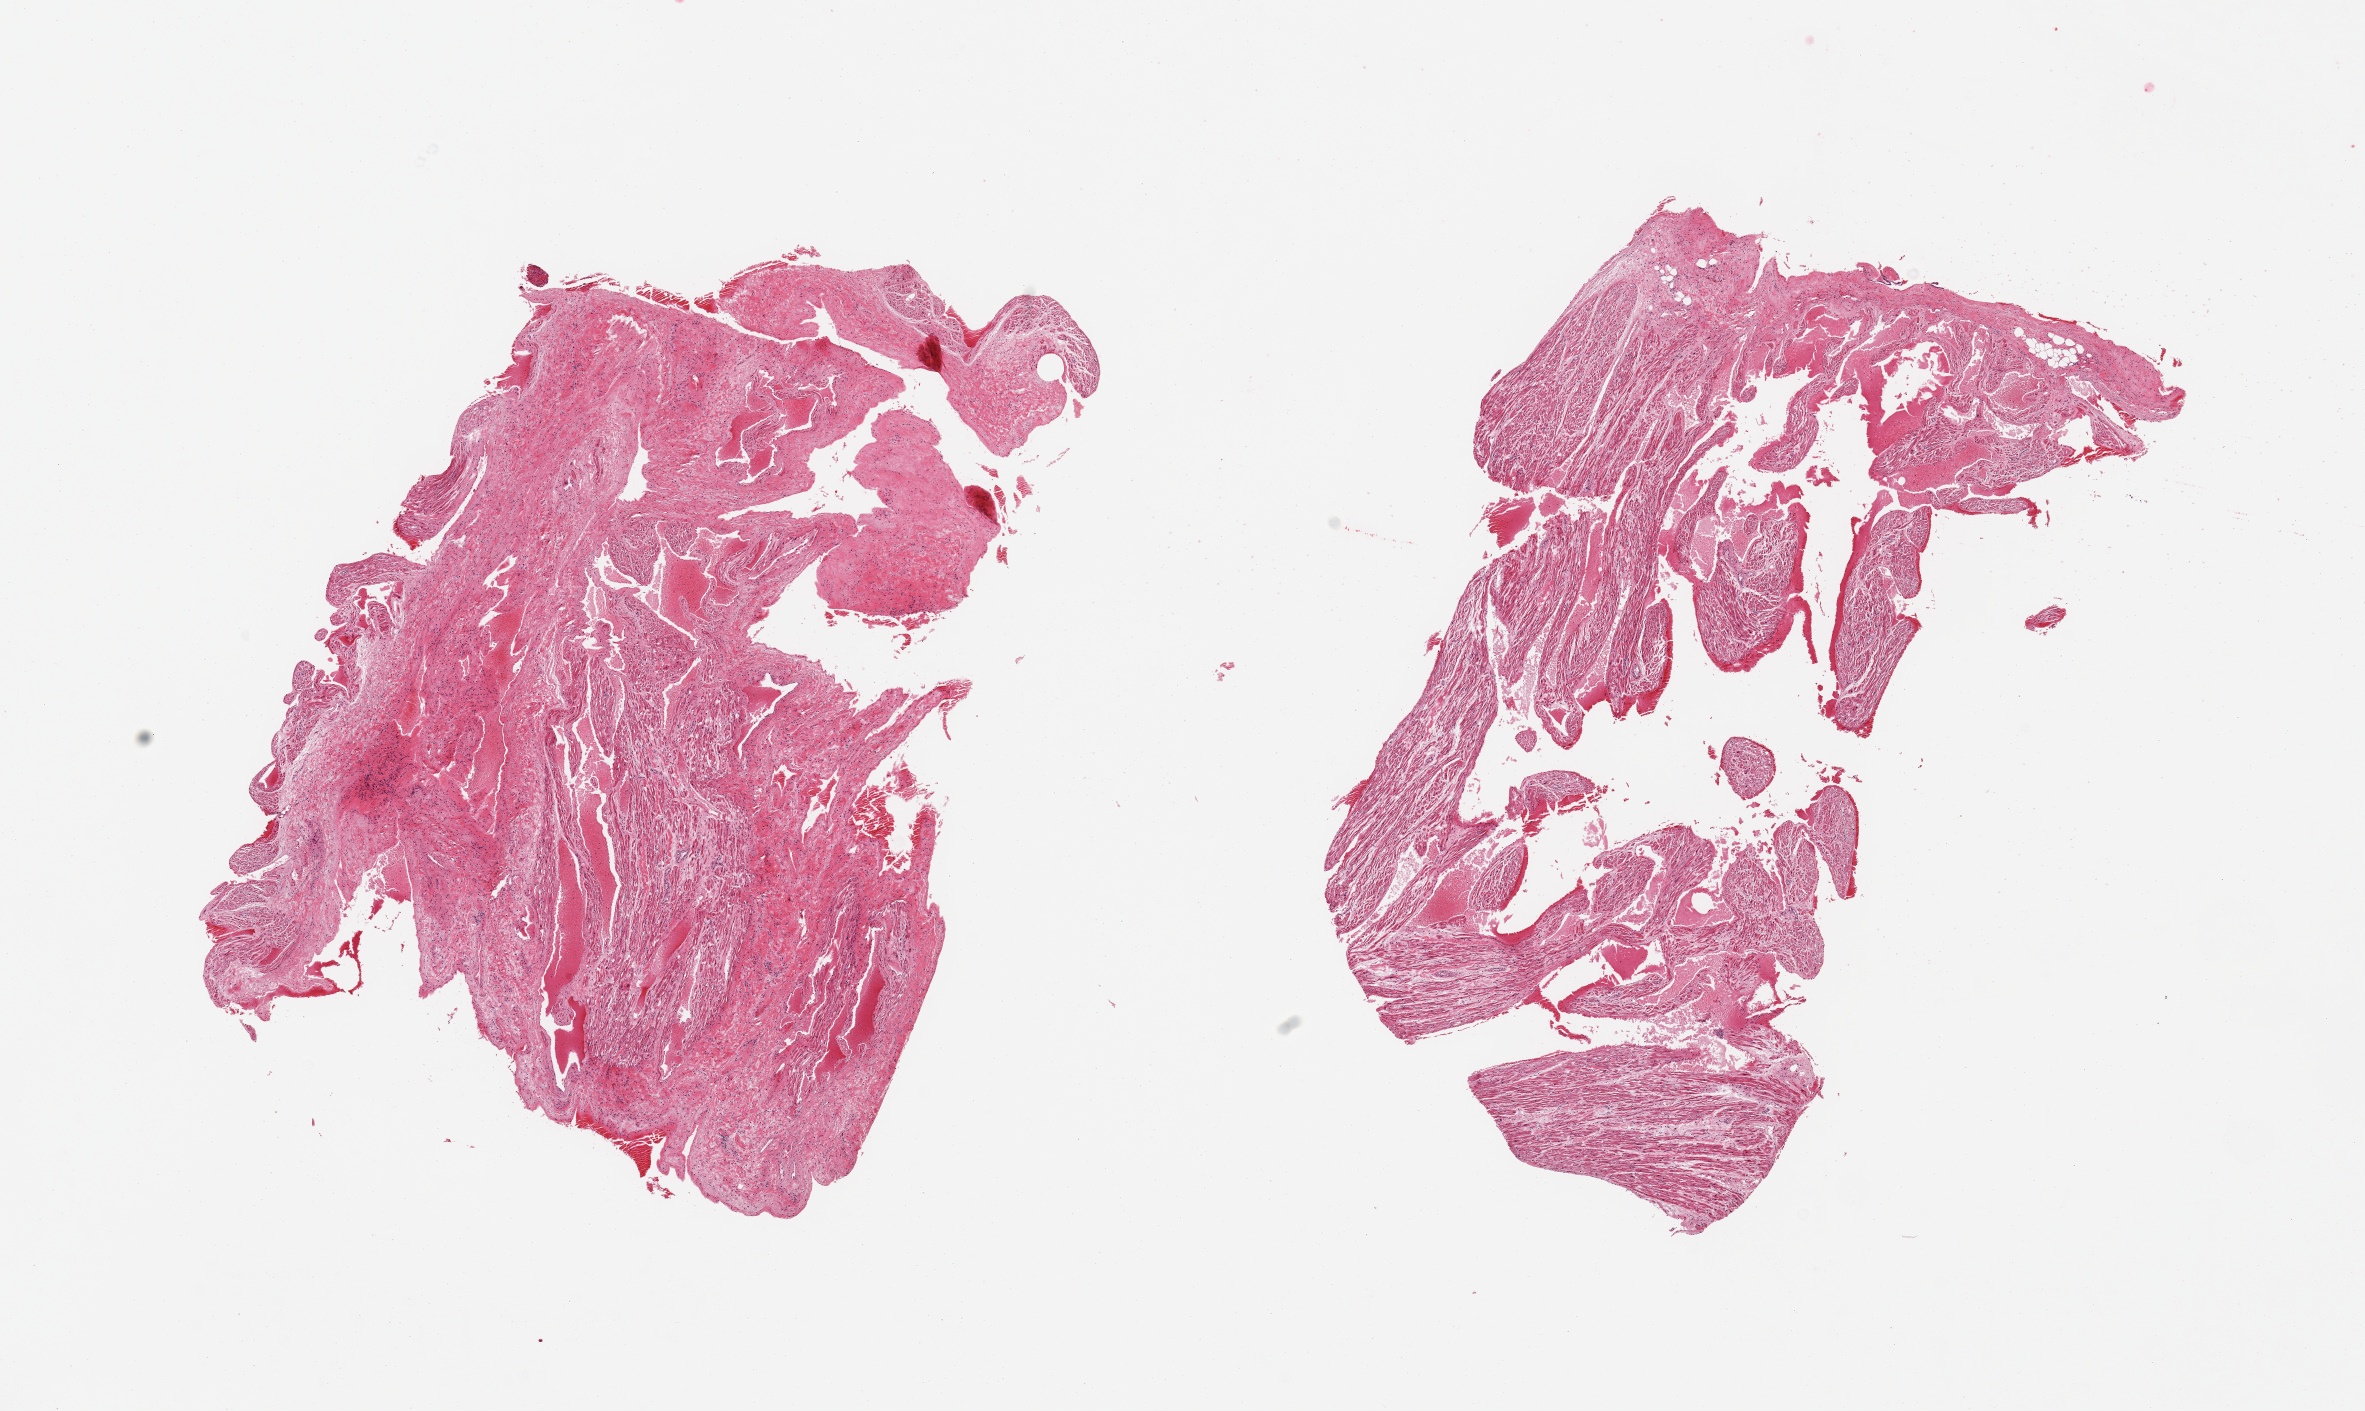
Digitized H&E-stained section, brightfield, low-resolution overview of the scanned area, about 18.7 x 11.2 mm. PAXgene-fixed paraffin-embedded (PFPE) section. Section of auricular appendage (target tissue). Donor tissue sample. Donor: male.
Review note (as recorded): 2 pieces, no abnormalities.